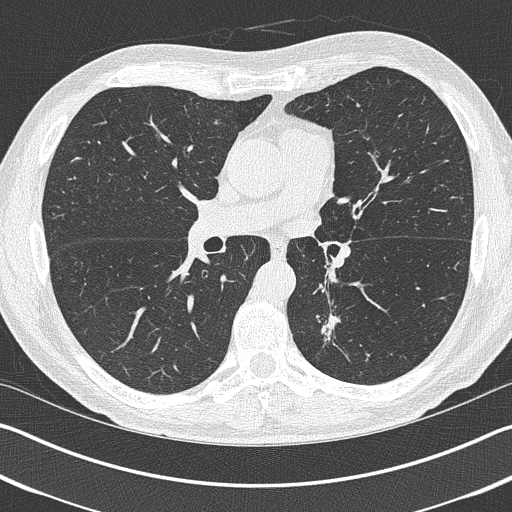
Chest CT (low-dose screening protocol), one axial image. Baseline annual screen. Lung window (W 1500 / L -600 HU). 512 × 512 image matrix. Male participant, aged 69 years at enrolment. Current smoker at enrolment.
Lesion marked by an expert reader, bounding box <294,304,351,362> (left, top, right, bottom; pixels). Reader record for this screening exam (exam-level; its link to the box is not recorded): non-calcified nodule or mass ≥4 mm, left upper lobe, 19 × 19 mm, spiculated (stellate) margins, pre-existing on the prior screen: yes. Official screen result: positive, change unspecified: nodule(s) >= 4 mm or enlarging nodule(s), mass(es), or other non-specific abnormalities suspicious for lung cancer. Lung cancer was diagnosed 202 days after this screen: non-small cell carcinoma, left lower lobe, stage IIIA (AJCC 6th edition), 20 mm at pathology.